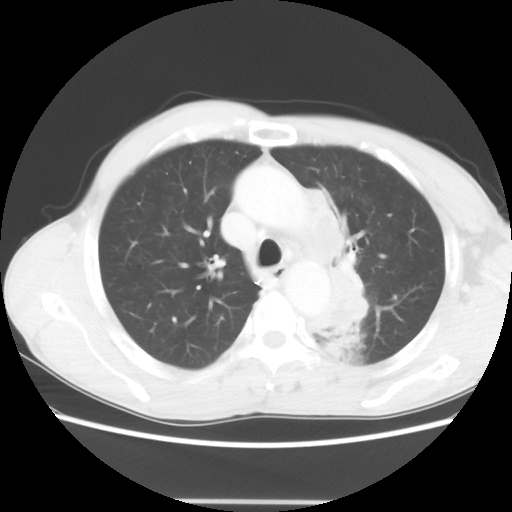
Chest CT, one axial slice; slice 46 of 62 in the series (ordered by position); reconstruction kernel STANDARD; 100 kVp; lung window (W 1500 / L -600 HU); 5 mm slice thickness; 512 × 512 image matrix, field of view 360 × 360 mm. Male patient, age 61 years. Case-level facts recorded for this patient, not image findings: clinical TNM (as recorded): T3 N1 M1.
Annotated regions visible in this slice (bounding box drawn by a radiologist):
- lung tumour (recorded histology: adenocarcinoma): box from (x=294, y=180) to (x=369, y=339) px